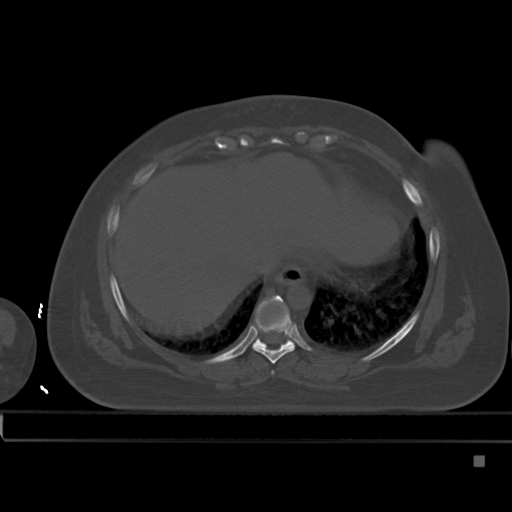
CT including the spine, one axial slice; position 272 of 495 along the scan axis; bone window (W 1800 / L 400 HU); 1.5 mm slice thickness; 512 × 512 image matrix, field of view 404 × 404 mm. Female patient, age 33 years. Case-level facts recorded for this patient, not image findings: primary cancer: breast.
Structures marked on this image (semi-automatically segmented with operator editing):
- T7 vertebra: box from (x=272, y=371) to (x=274, y=373) px
- T8 vertebra: (x=253, y=295)–(x=295, y=364)
- T9 vertebra: (x=253, y=295)–(x=294, y=348)